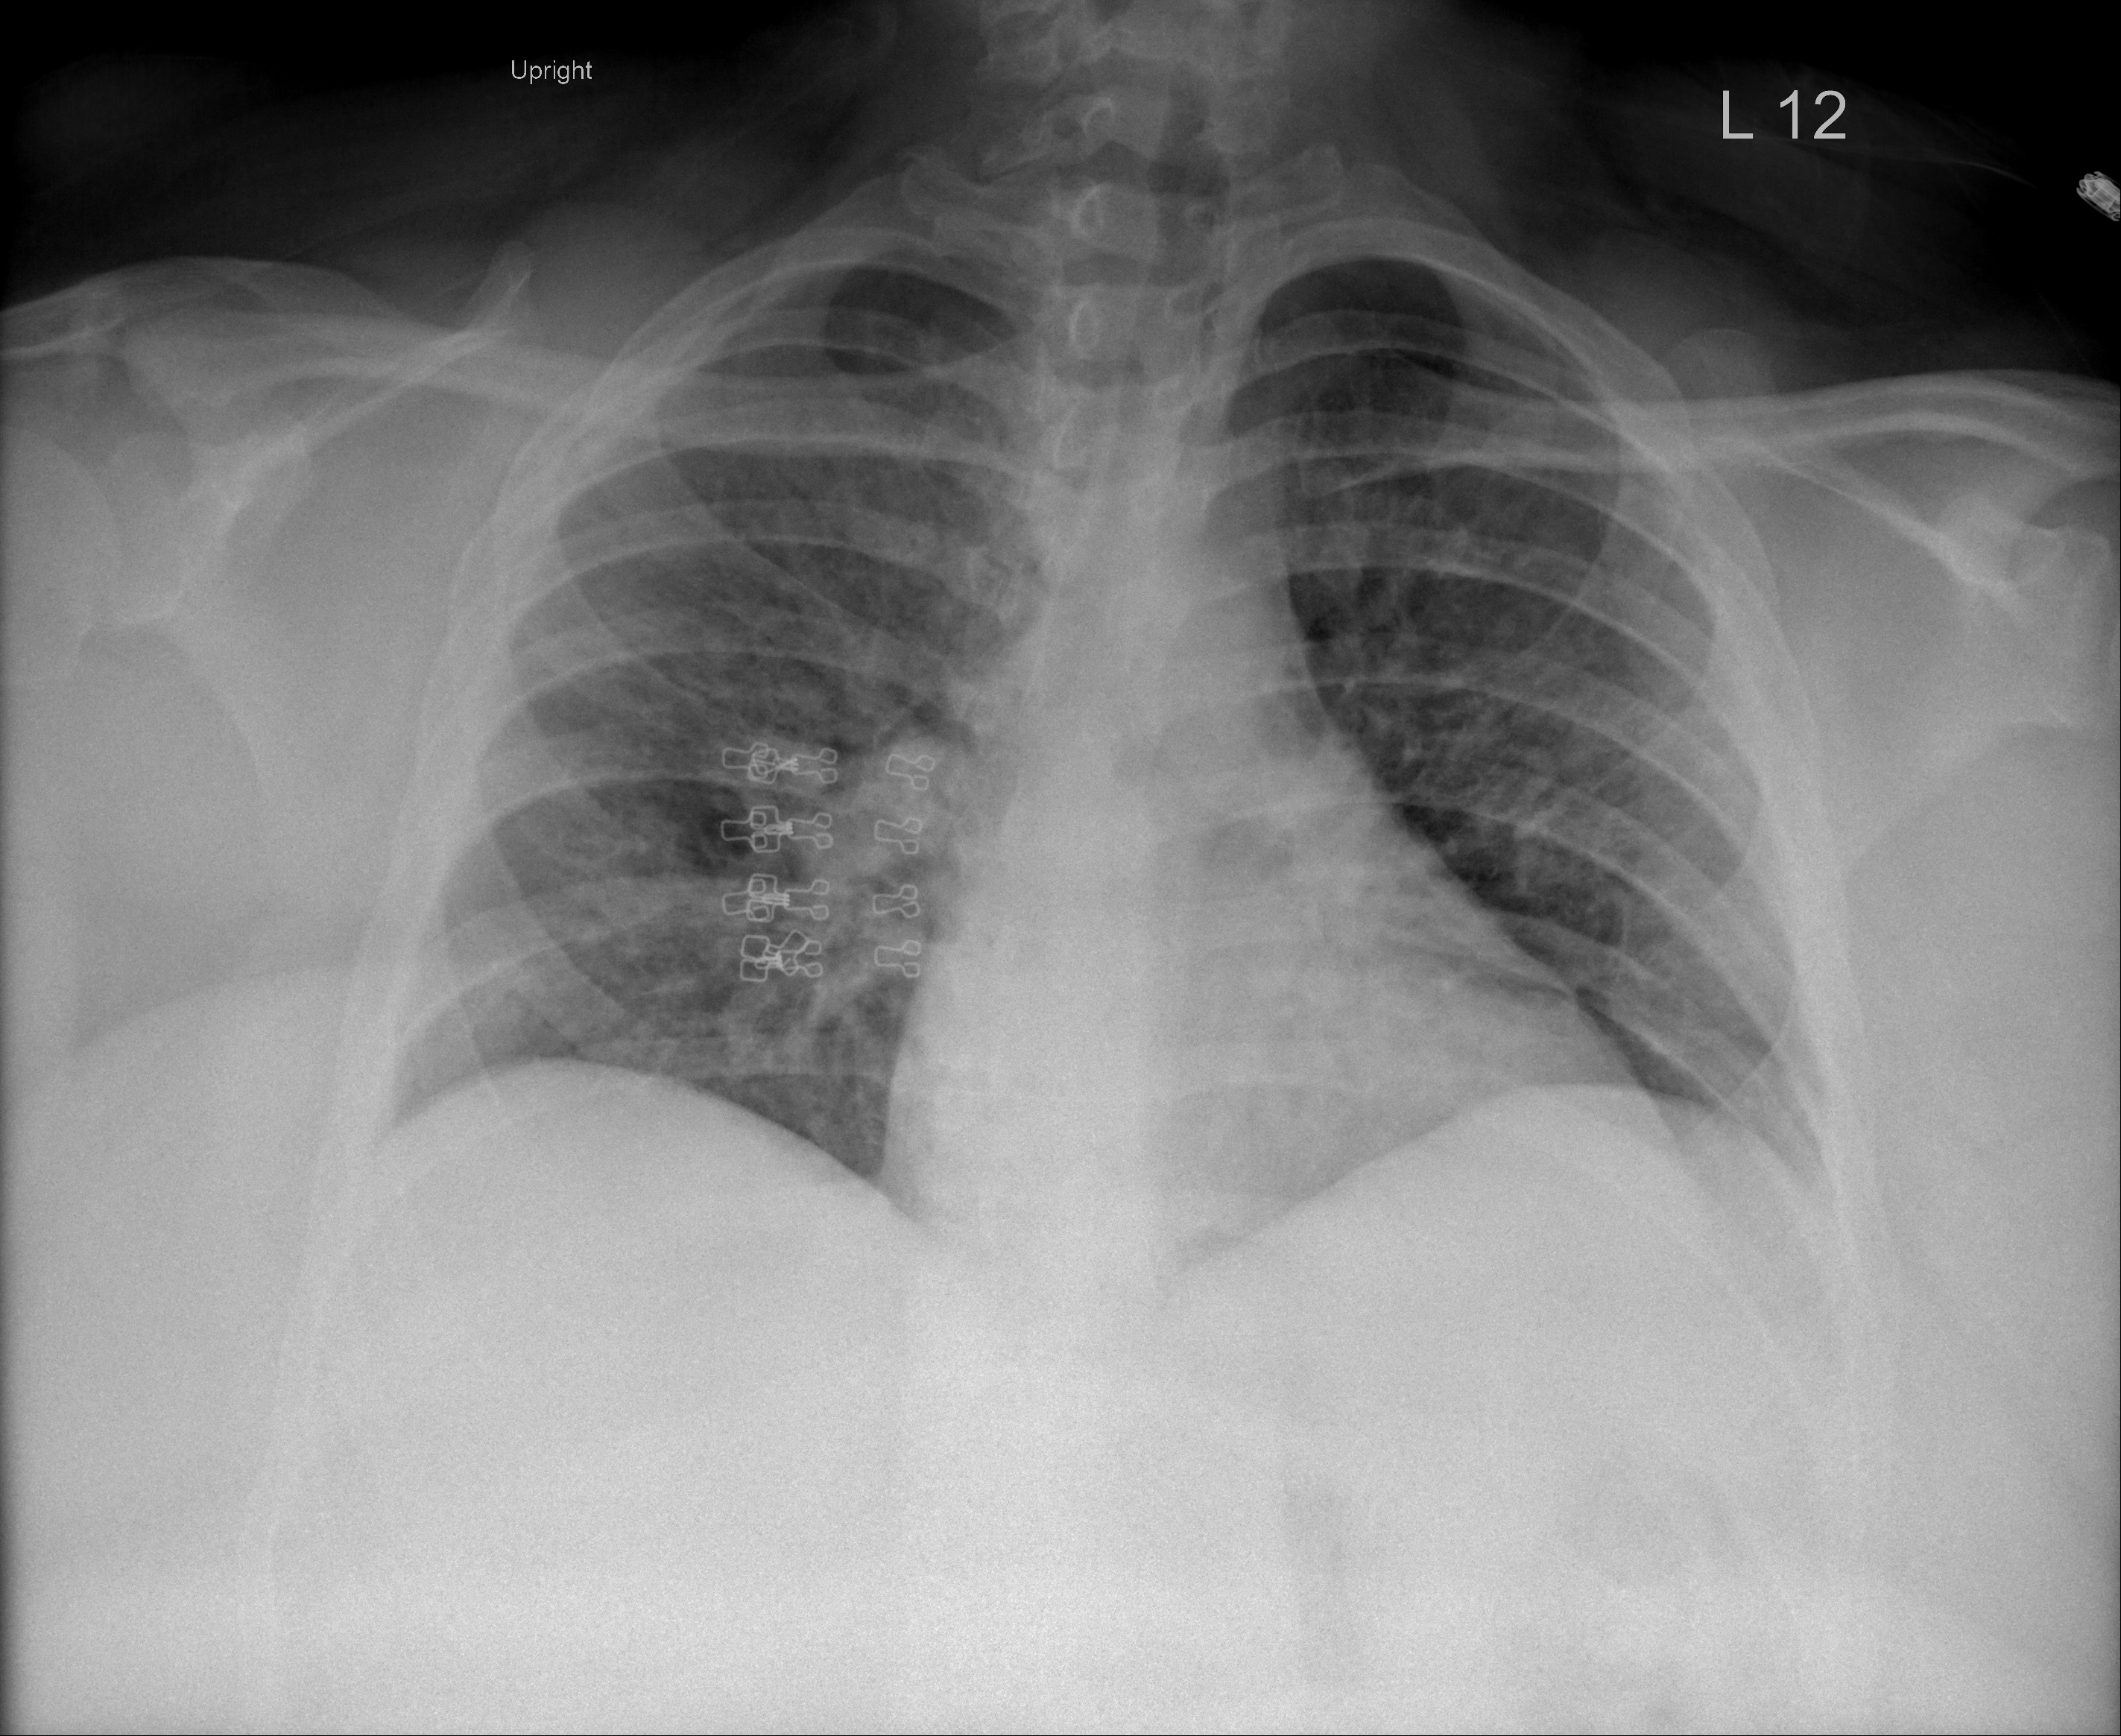
Chest X-ray, AP projection. Female patient, age 44 years; imaged 2 days after the COVID-19 diagnosis.
Key findings recorded by the radiologist: Lung volumes remain low but there appears to have been clearing since prior radiograph.